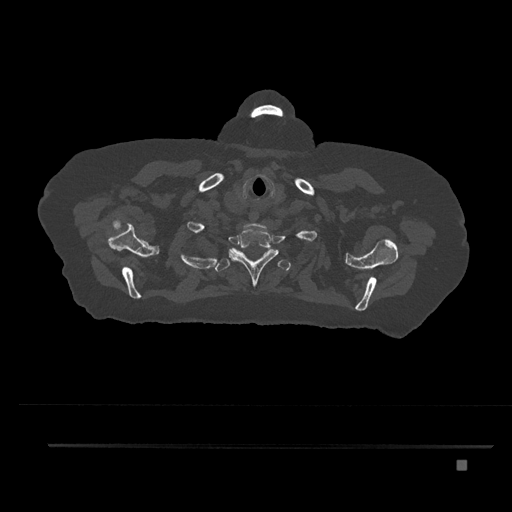
CT including the spine, one axial slice; slice 692 of 797 in the series (ordered by position); reconstruction kernel Br40s/3; bone window (W 1800 / L 400 HU); 0.5 mm slice thickness; 512 × 512 image matrix. Patient: female, 76 years. From the clinical record (not read from this slice): primary cancer: lung; vertebrae with lytic lesions (as recorded): T11, L3.
Structures marked on this image (semi-automatic segmentation, software-assisted and operator-edited):
- T1 vertebra: bounding box (x1, y1, x2, y2) in pixels: (229, 227, 279, 287)
- T2 vertebra: (207, 248, 291, 272)